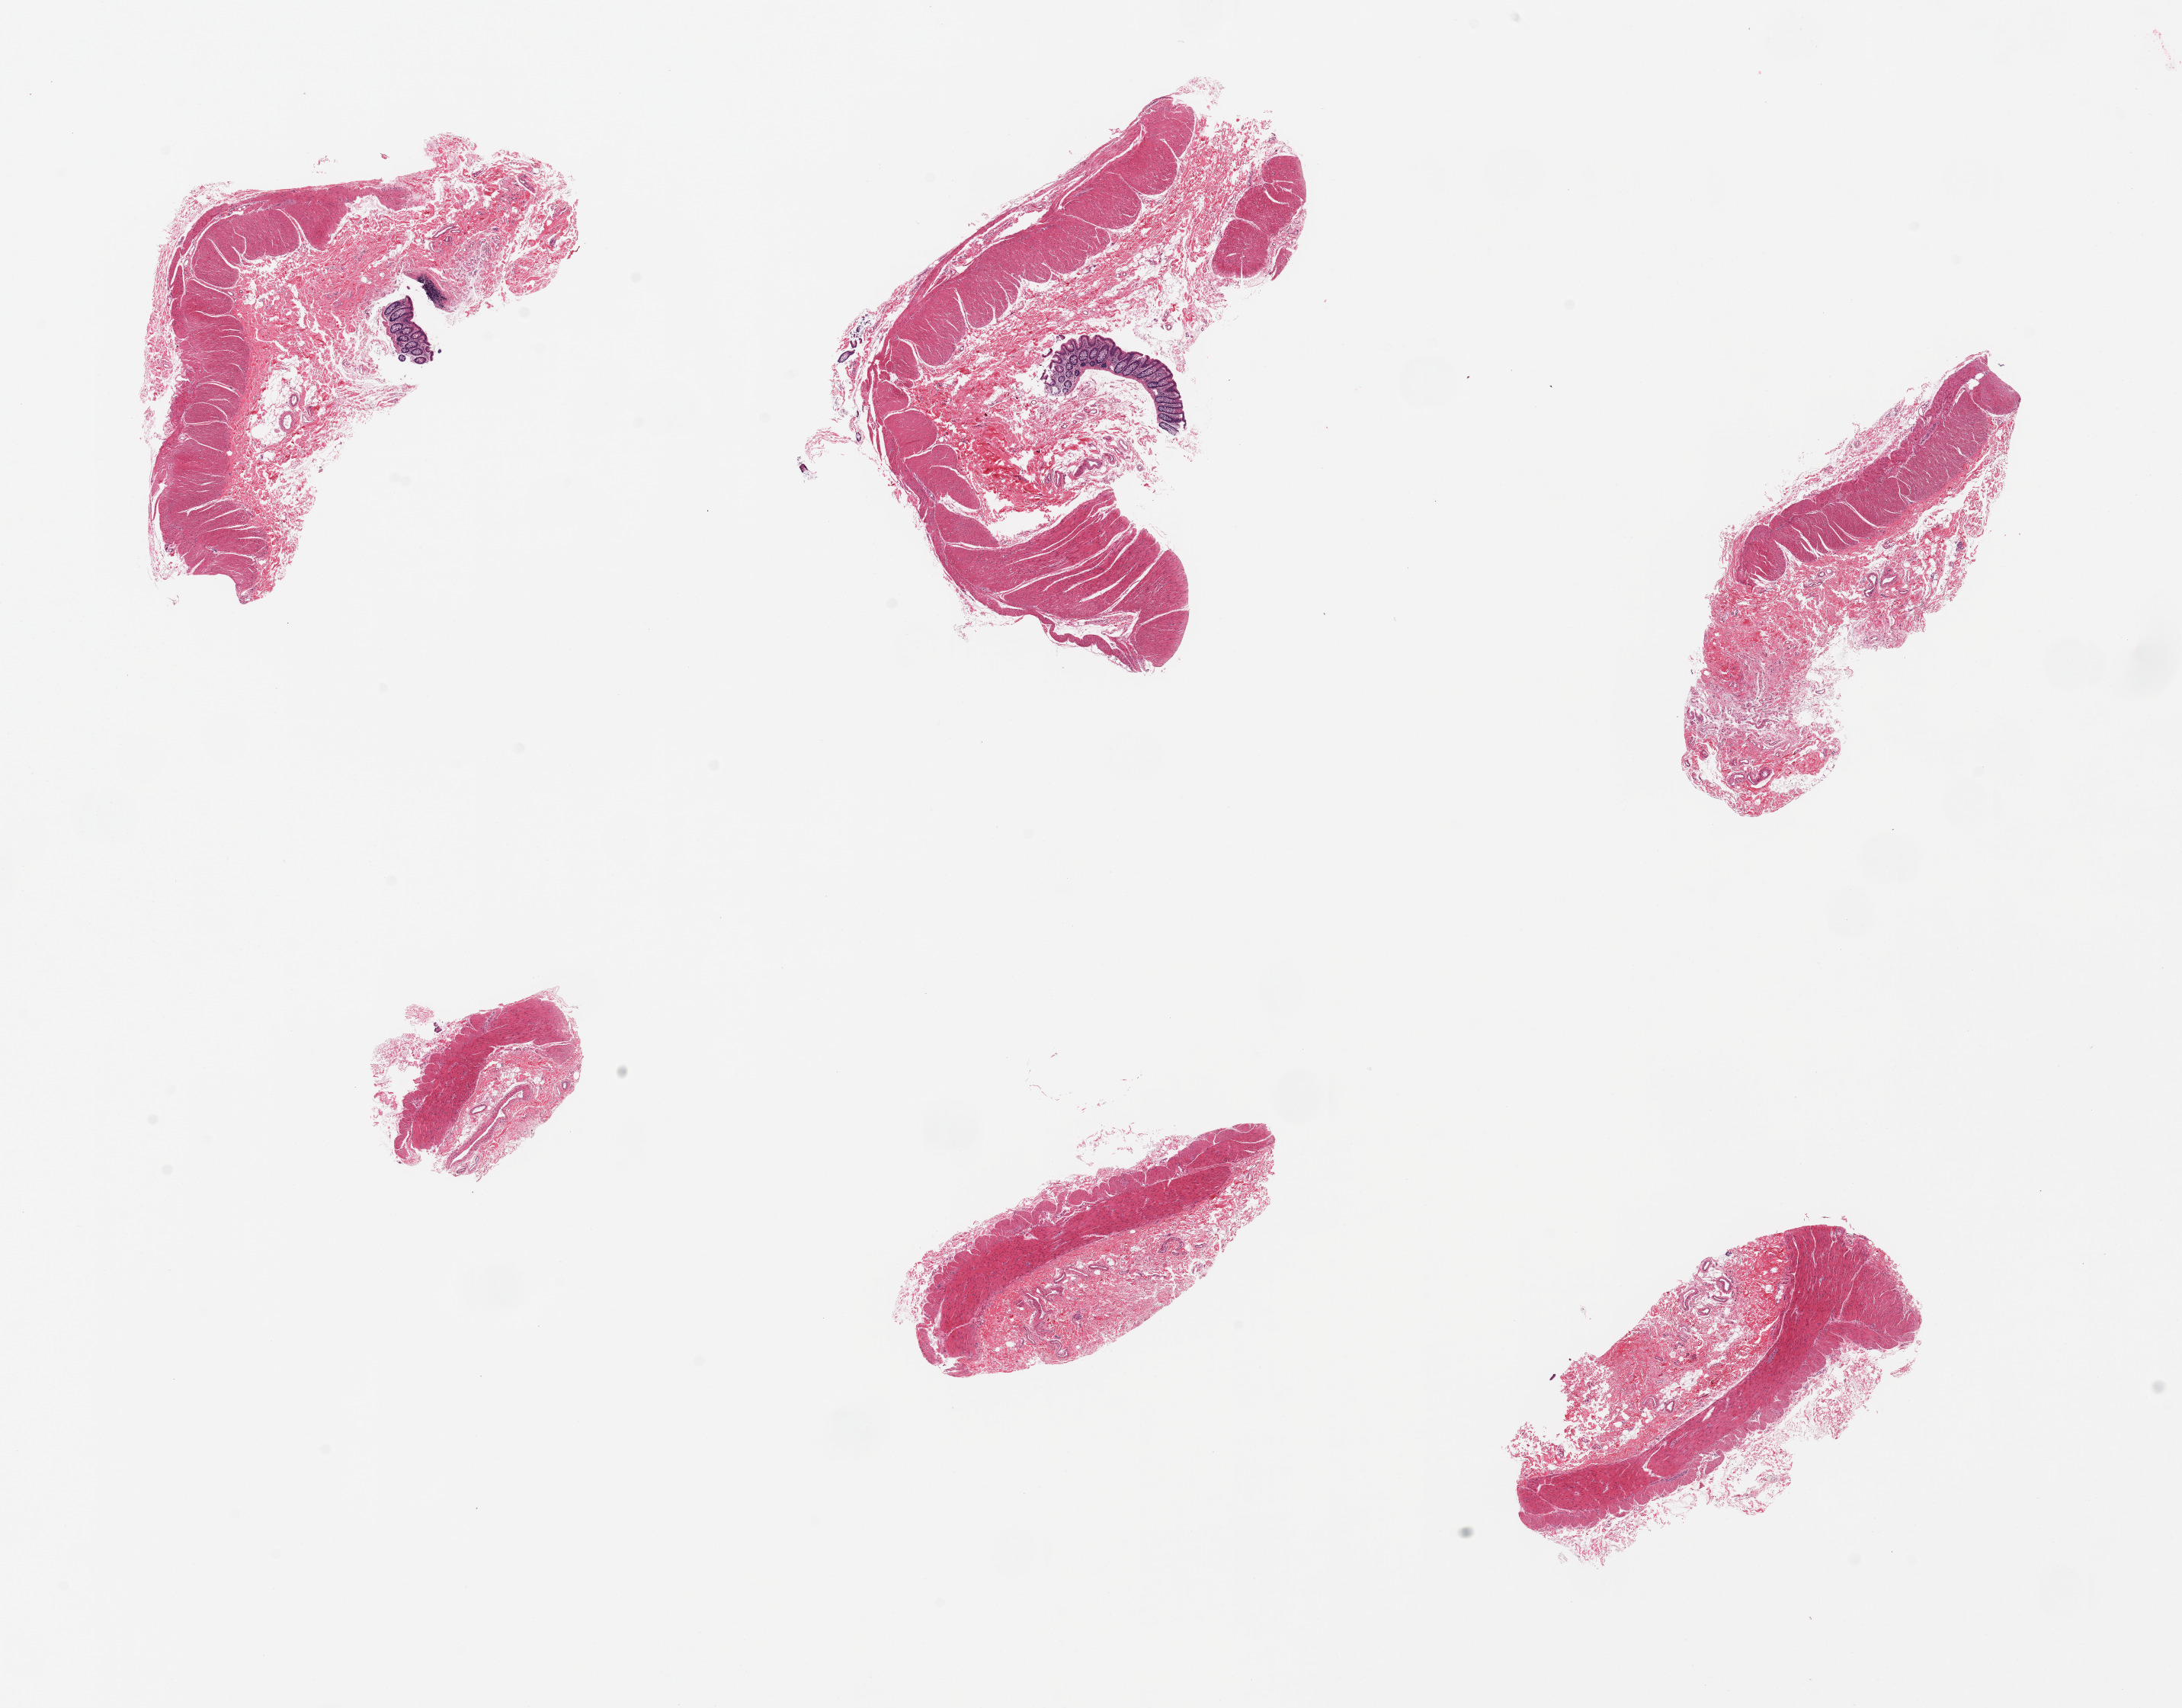
Digitized H&E-stained section — low-resolution overview of the scanned area, about 22.6 x 17.7 mm (slide scanned at 20x). PAXgene-fixed, paraffin-embedded tissue. Section of sigmoid colon (target tissue). Donor tissue sample. Donor: male.
* review note (as recorded): 6 pieces, all muscularis, a few 'floaters' of mucosa